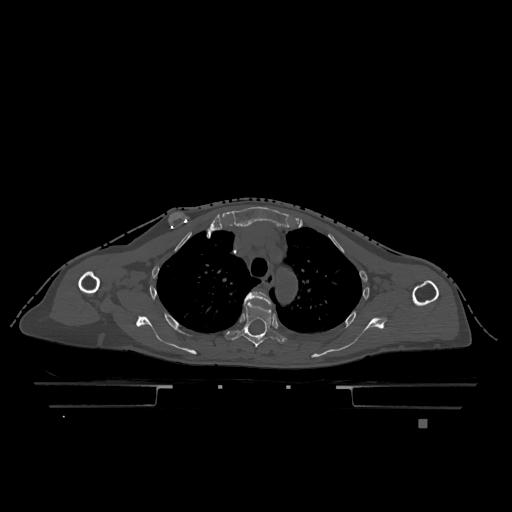
CT including the spine, one axial slice; bone window (W 1800 / L 400 HU); 0.5 mm slice thickness; 512 × 512 image matrix, field of view 500 × 500 mm. Patient: female, 74 years. Case-level facts recorded for this patient, not image findings: primary cancer: lung.
Structures marked on this image (semi-automatically segmented with operator editing):
- T3 vertebra: bounding box [x1, y1, x2, y2] px = [244, 291, 271, 305]
- T4 vertebra: [224, 302, 287, 347]